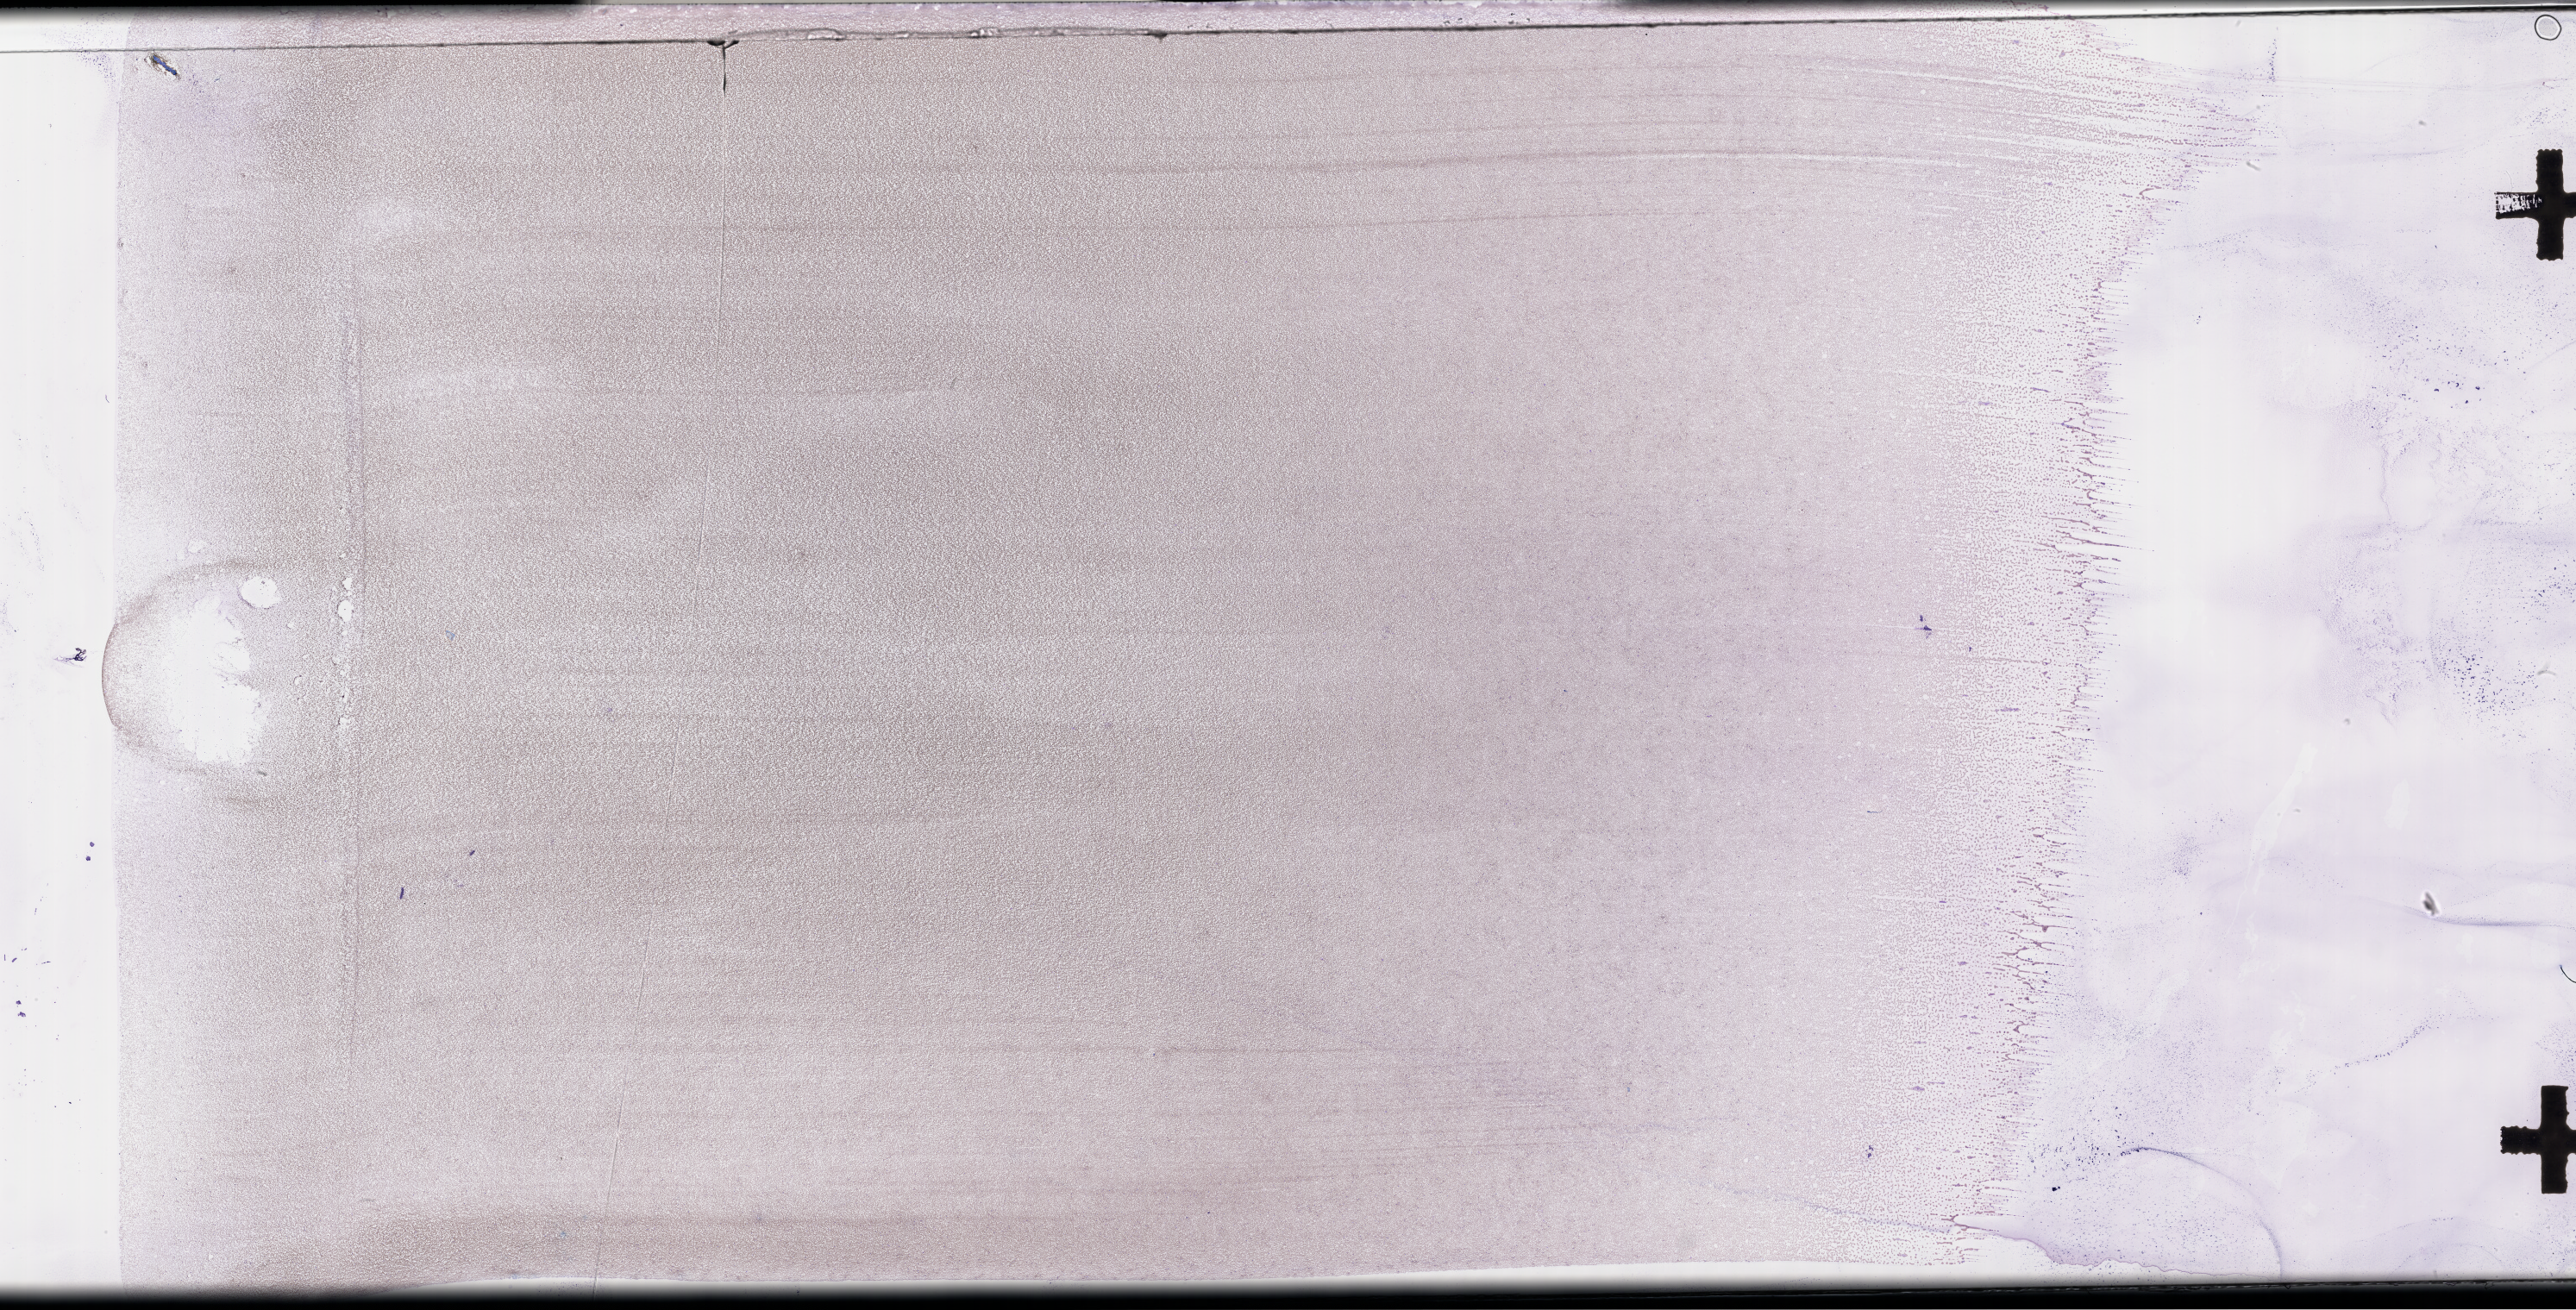
Wright-Giemsa-stained whole blood smear, whole-slide image, shown as a low-resolution overview of the whole scanned area (about 48.2 x 24.5 mm). EDTA-anticoagulated smear. Collected on treatment. Patient sex: male.
* from a patient with: Plasma Cell Myeloma